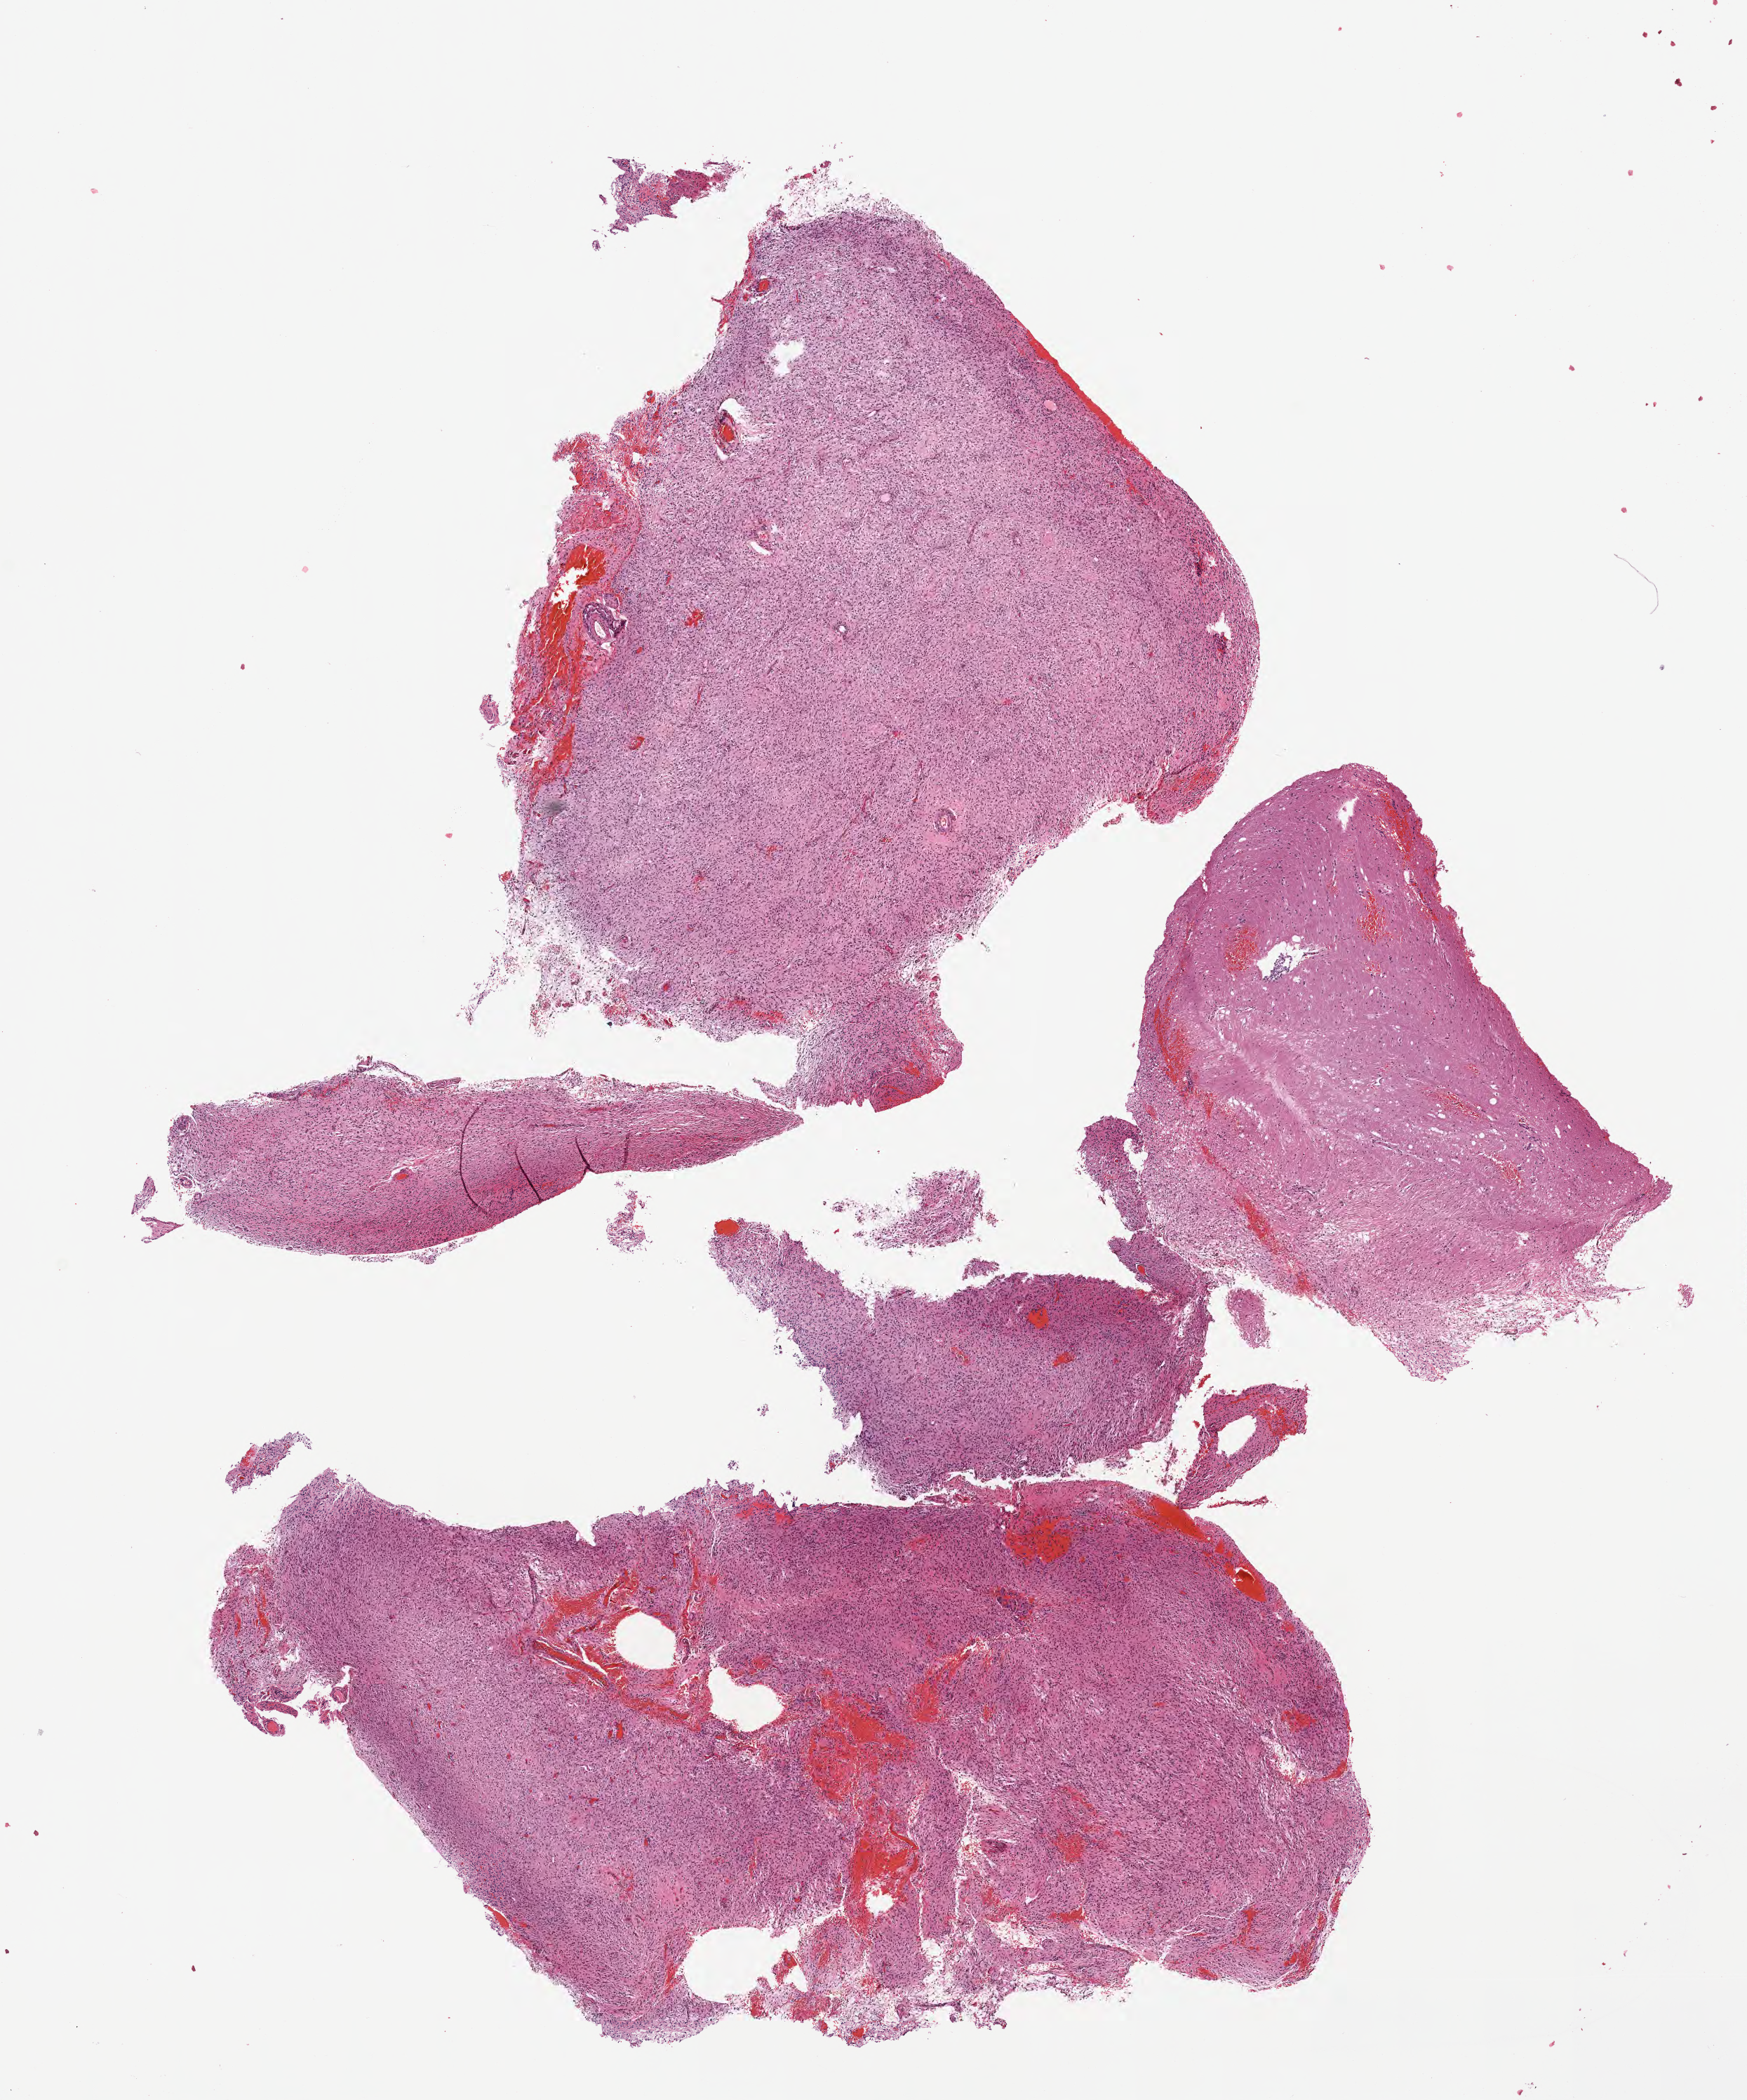
Digitized haematoxylin and eosin-stained section of tumor tissue from the brain — shown as a low-resolution overview of the whole scanned area (about 10.1 x 12.1 mm), formalin-fixed paraffin-embedded section. Patient: male, age 174 months.
Diagnosis (ICD-O-3 morphology term): Pilocytic astrocytoma.